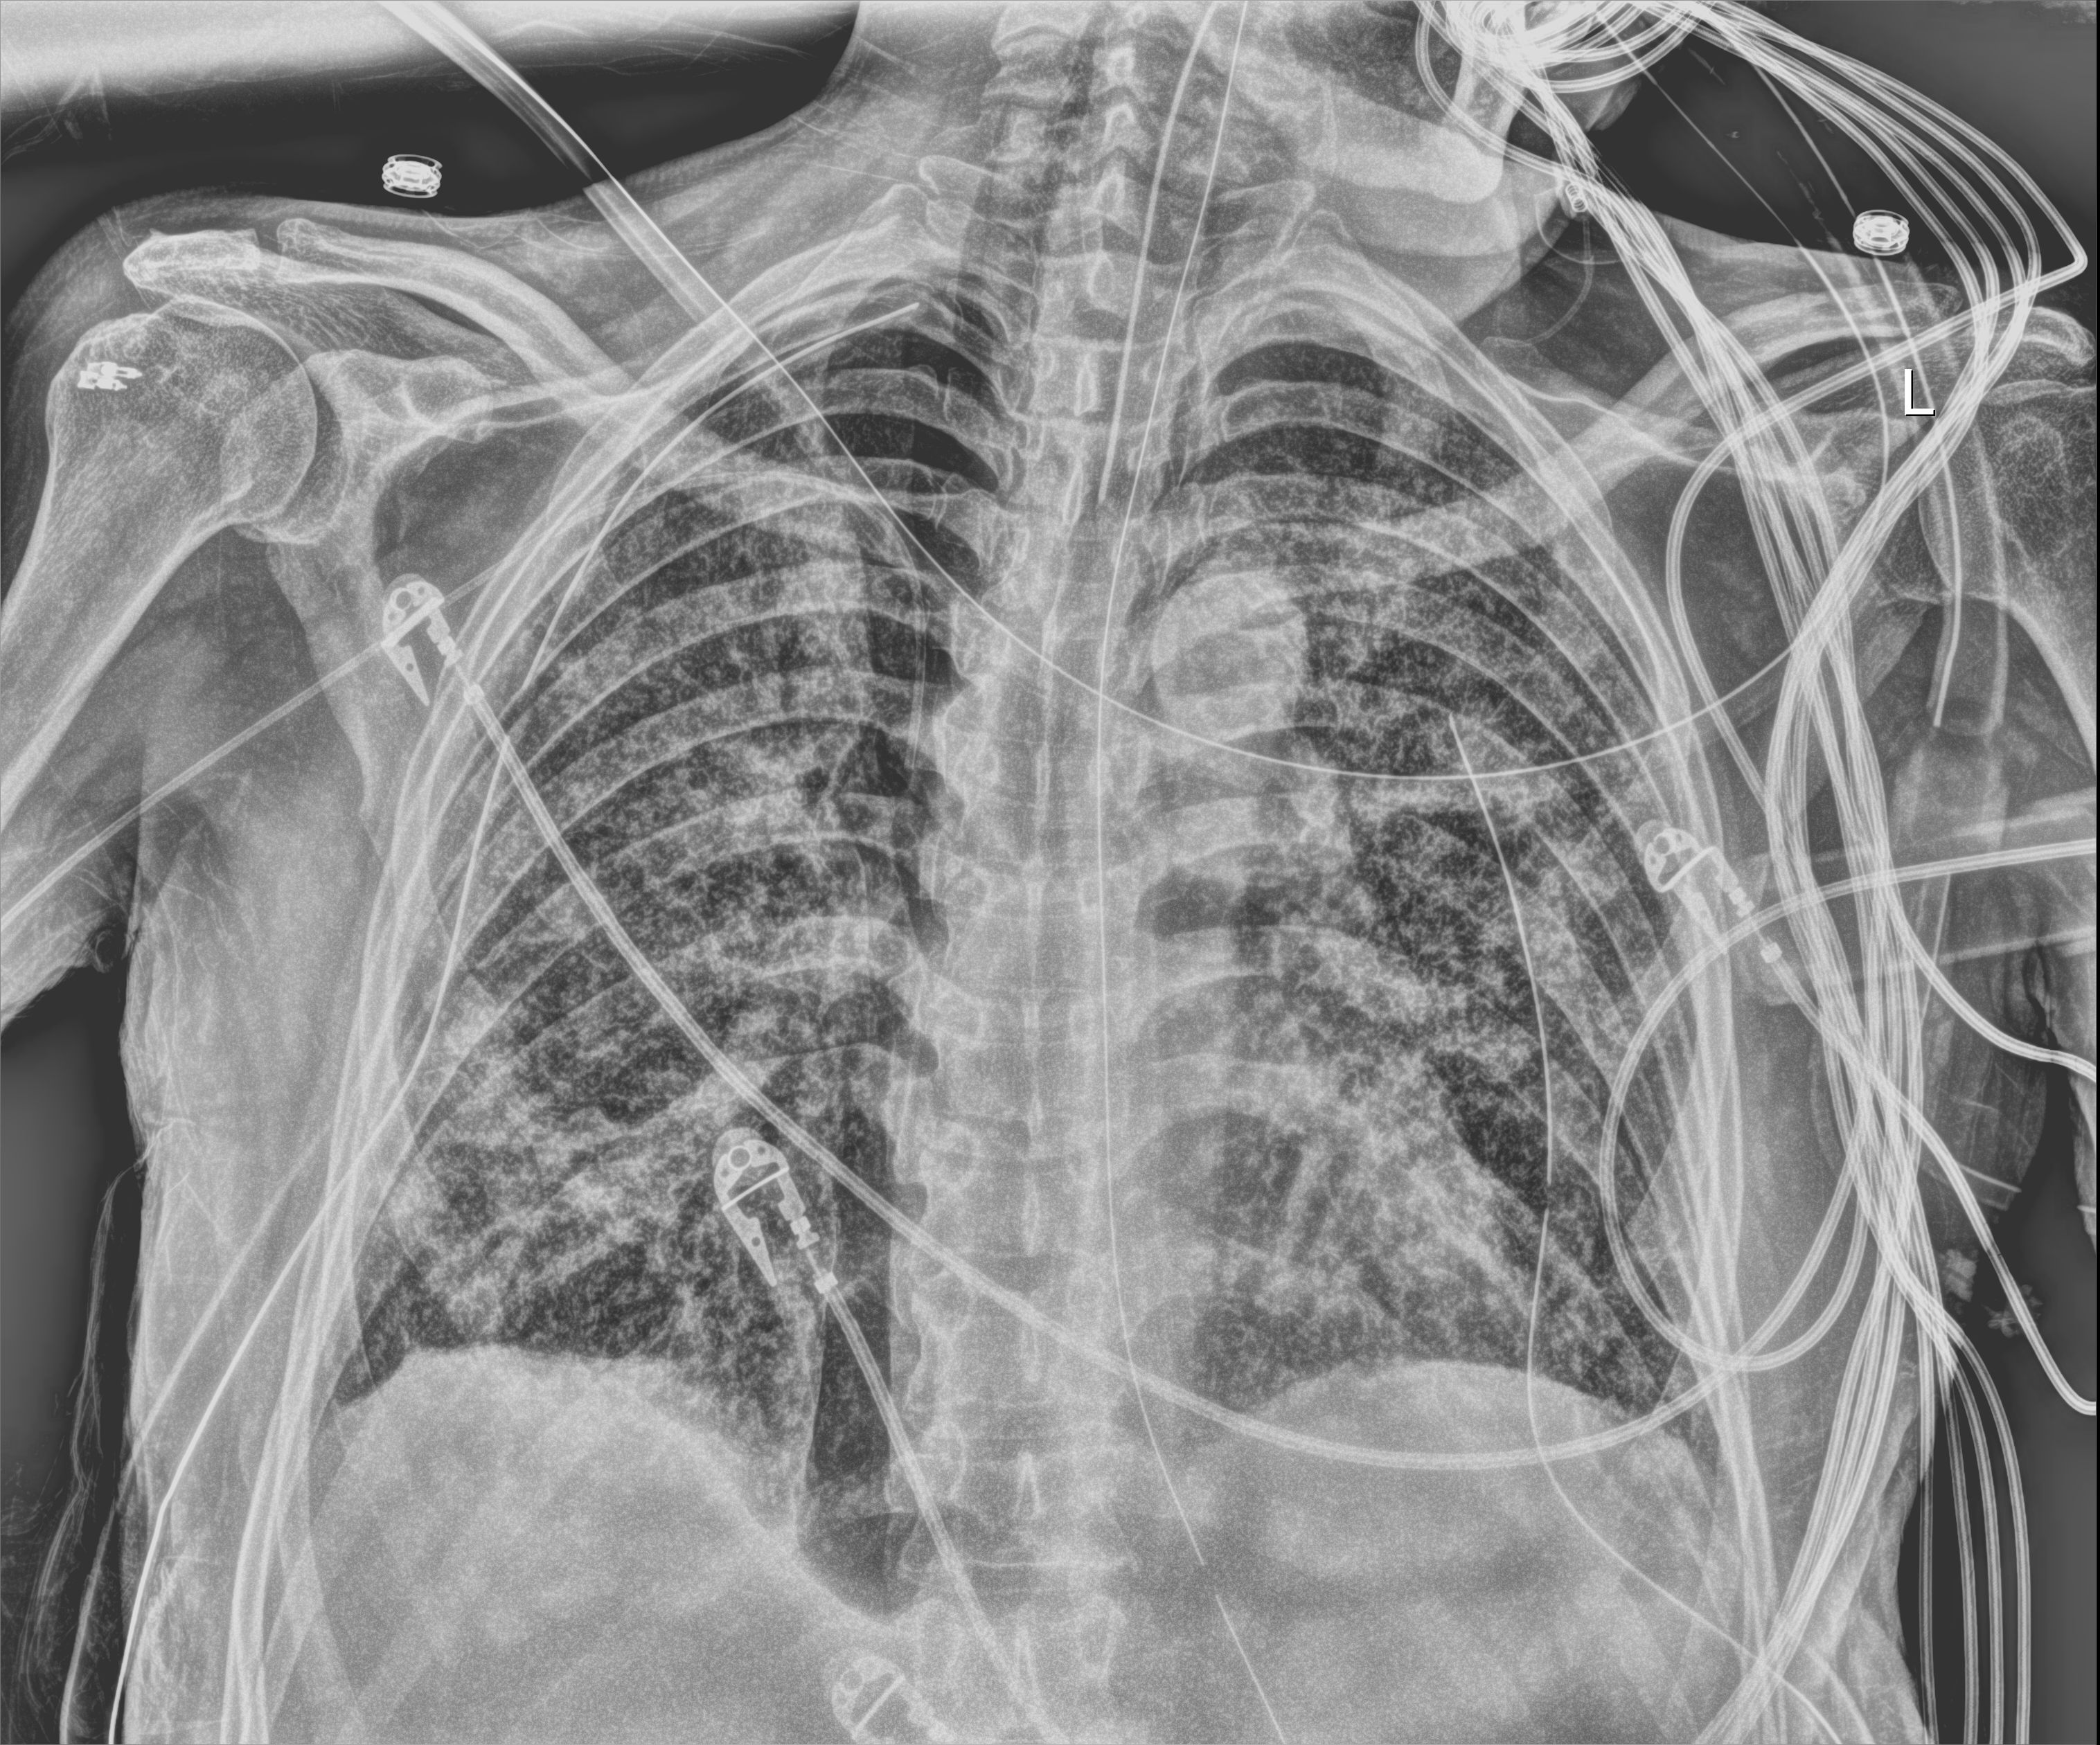
Portable chest radiograph; anteroposterior (AP) projection. Patient hospitalised with COVID-19; male, aged 60–74 years.
Admission-level facts for this patient (not findings on this image; timing relative to this image not recorded):
- smoking status (admission record): never
- admitted to intensive care during this hospital stay: yes
- other chronic lung disease (admission record): yes